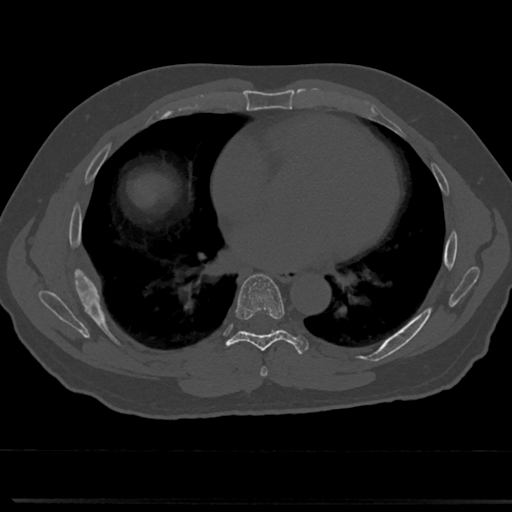
CT including the spine, one axial slice. Slice 404 of 817 in the series (ordered by position). Bone window (W 1800 / L 400 HU). 0.5 mm slice thickness. 512 × 512 image matrix. Patient: male, 61 years. Case-level facts recorded for this patient, not image findings: primary cancer: prostate.
Outlined on this slice (semi-automatic segmentation, software-assisted and operator-edited):
- T6 vertebra: bounding box <260,340,319,373> (left, top, right, bottom; pixels)
- T7 vertebra: <215,275,309,358>